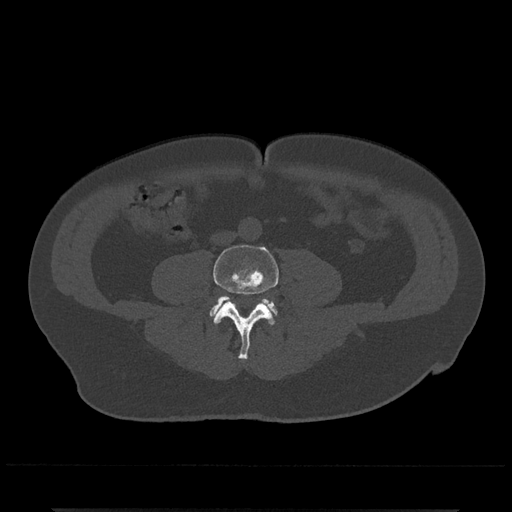
CT including the spine, one axial slice. Slice 141 of 797 in the series (ordered by position). Reconstruction kernel Br40s/3. 120 kVp. Bone window (W 1800 / L 400 HU). 0.5 mm slice thickness. 512 × 512 image matrix, field of view 393 × 393 mm. Patient: male, 67 years. From the clinical record (not read from this slice): primary cancer: prostate.
Structures marked on this image (semi-automatically segmented with operator editing):
- L4 vertebra: bounding box <213,244,279,360> (left, top, right, bottom; pixels)
- L5 vertebra: <210,296,277,319>